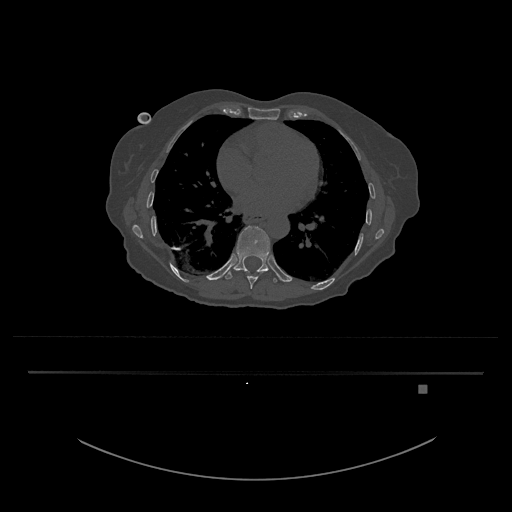
CT including the spine, one axial slice; reconstruction kernel Br40s/3; 120 kVp; bone window (W 1800 / L 400 HU); 0.5 mm slice thickness; 512 × 512 image matrix, field of view 500 × 500 mm. Female patient, age 57 years. Case-level facts recorded for this patient, not image findings: primary cancer: cervical.
Annotated regions visible in this slice (semi-automatic segmentation, software-assisted and operator-edited):
- T10 vertebra: bounding box <224,226,278,283> (left, top, right, bottom; pixels)
- T9 vertebra: <247,276,257,289>